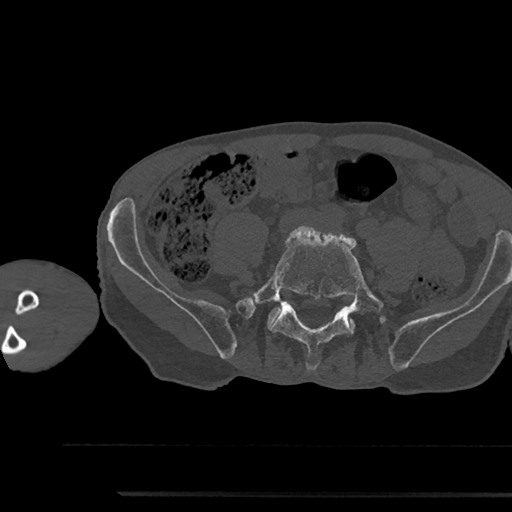
CT including the spine, one axial slice. Reconstruction kernel Br40s/3. 120 kVp. Bone window (W 1800 / L 400 HU). 0.5 mm slice thickness. 512 × 512 image matrix, field of view 367 × 367 mm. Male patient, age 79 years. From the clinical record (not read from this slice): primary cancer: prostate.
Structures marked on this image (semi-automatic segmentation, software-assisted and operator-edited):
- L5 vertebra: bounding box (x1, y1, x2, y2) in pixels: (252, 226, 383, 370)